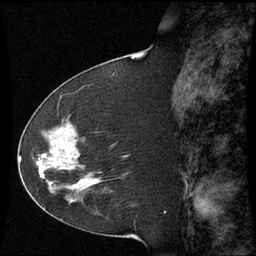
Breast MRI (dynamic contrast-enhanced), one sagittal slice; position 26 of 60 along the scan axis; dynamic contrast-enhanced series, image 2 of 3 at this slice position (ordered by acquisition); 1.5 T; TE 4.2 ms, TR 8.9 ms; 2.3 mm slice thickness; 256 × 256 image matrix, field of view 210 × 210 mm. Female patient, age 51 years. Case-level facts recorded for this patient, not image findings: setting: breast cancer imaged before/during neoadjuvant chemotherapy; receptor status: HR-positive, HER2-negative.
Structures marked on this image (semi-automatic segmentation, software-assisted and operator-edited):
- analysis volume of interest (the breast-tissue region the enhancement analysis was run in; not a lesion): bounding box [x1, y1, x2, y2] px = [50, 121, 102, 187]
- tumour enhancement mask (voxels above the 70 % enhancement threshold inside the analysis volume of interest): [51, 130, 98, 183]